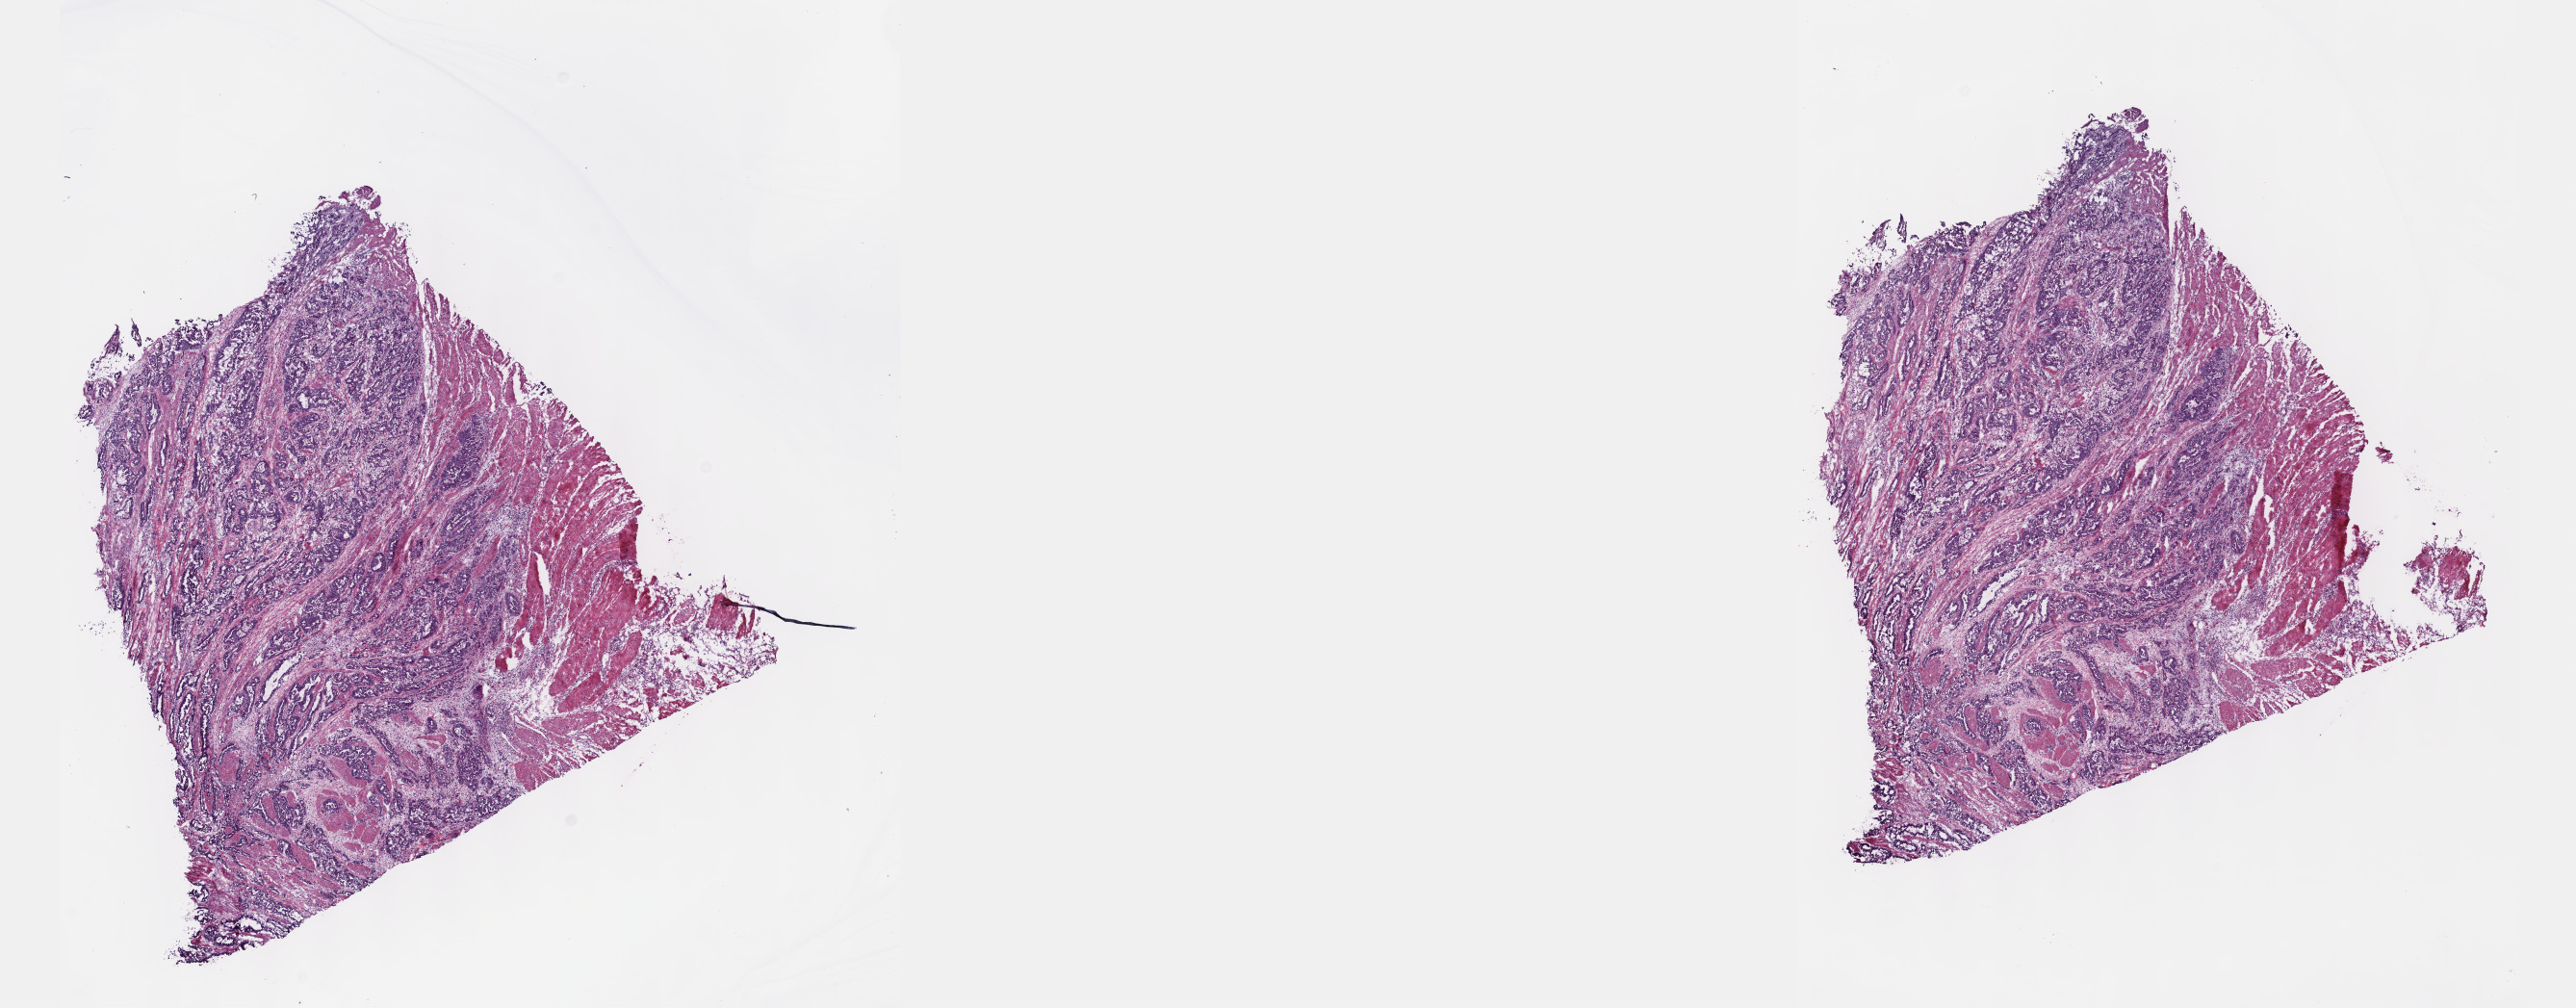
Whole-slide histology image, H&E-stained — shown as a low-resolution overview of the whole scanned area (about 21.6 x 8.5 mm, acquisition: 40x scan); frozen section from the top of the tissue portion; sample: primary tumour, esophagus. Patient: female, age at initial diagnosis 81 years. Histologic grade: GX (grade cannot be assessed). Slide review estimates, as recorded: tumour cells 97%, tumour nuclei 65%, normal cells 0%, stromal cells 0%, necrosis 3%. Infiltration values recorded for this section: lymphocyte infiltration 5%, monocyte infiltration 0%, neutrophil infiltration 1%.
- TNM: T3 N1 M0
- AJCC pathologic stage: III
- lymph nodes positive (case pathology): 7 of 10 examined
- diagnosis: Adenocarcinoma, NOS (lower third of esophagus)